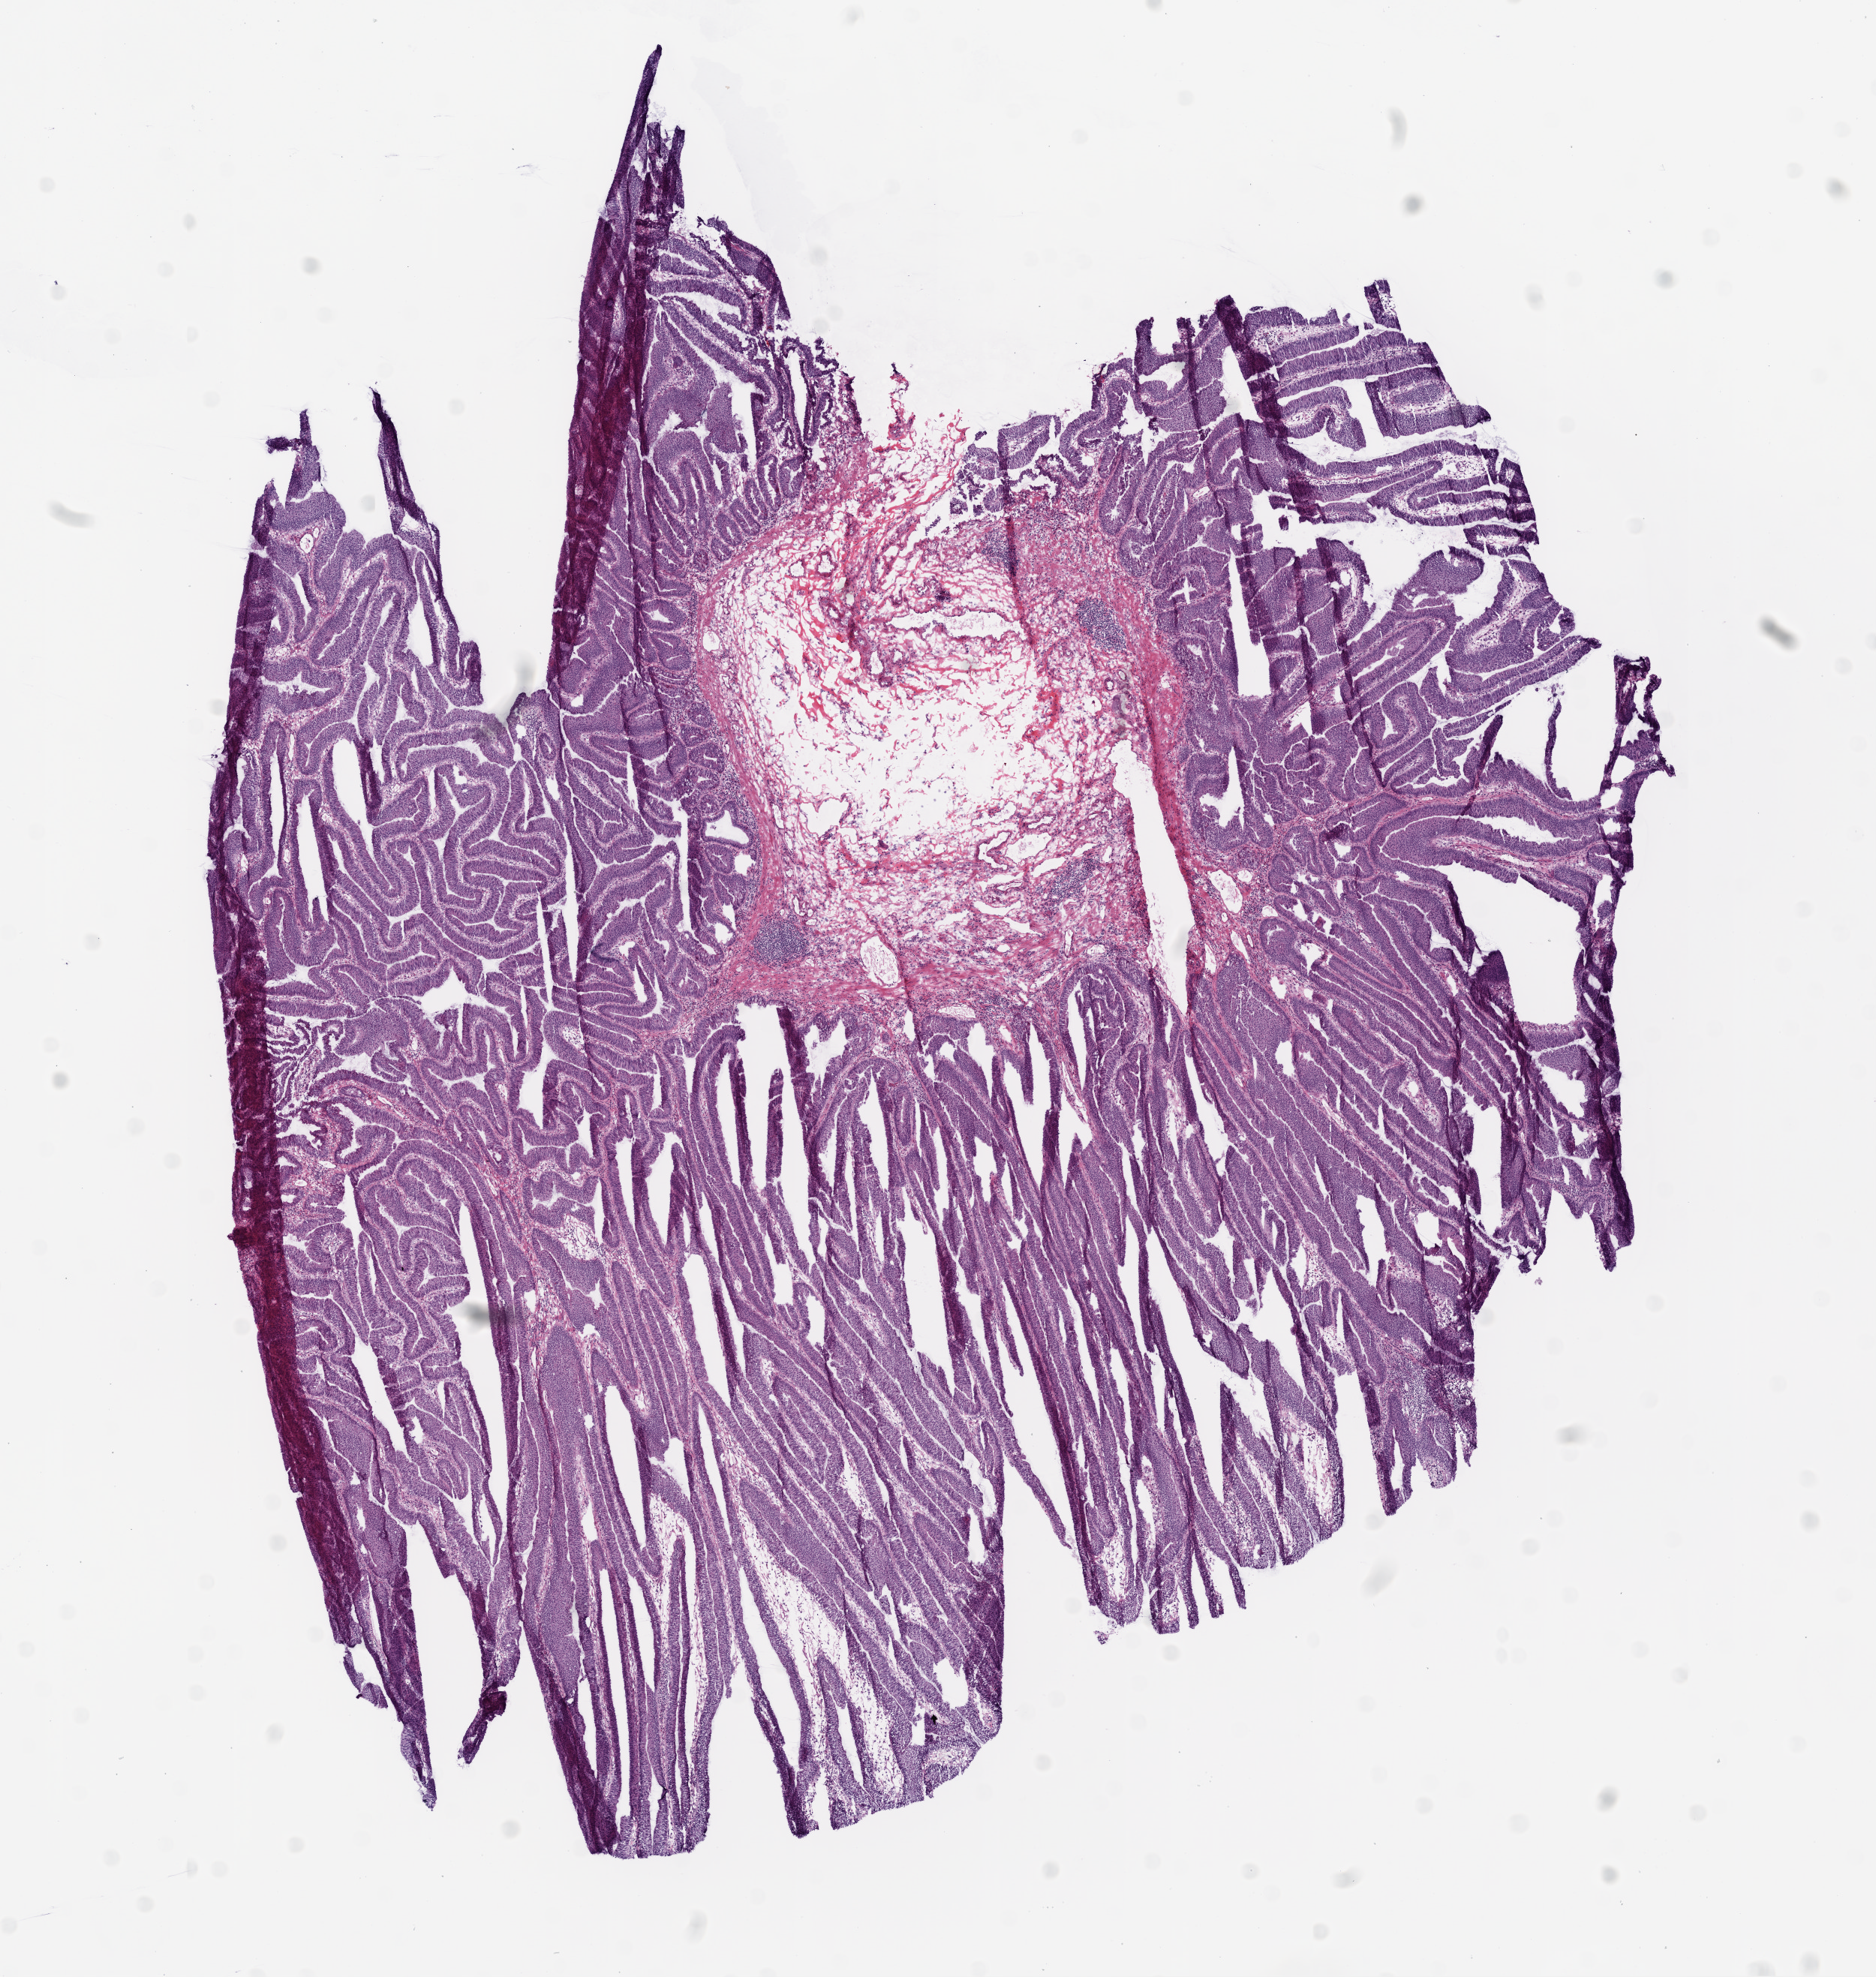
Digitized Hematoxylin and eosin (H&E) stained tissue section (whole slide) — whole scanned area (about 10.0 x 10.6 mm, acquisition: 20x scan) shown as a low-resolution overview, frozen section from the bottom of the tissue portion, colon, primary tumour sample. Male patient; age at initial diagnosis 73 years. Composition of this section per pathologist review: tumour cells 80%, tumour nuclei 80%, normal cells 0%, stromal cells 20%, necrosis 0%.
Histologic diagnosis: Adenocarcinoma, NOS. AJCC pathologic stage: I (5th edition).